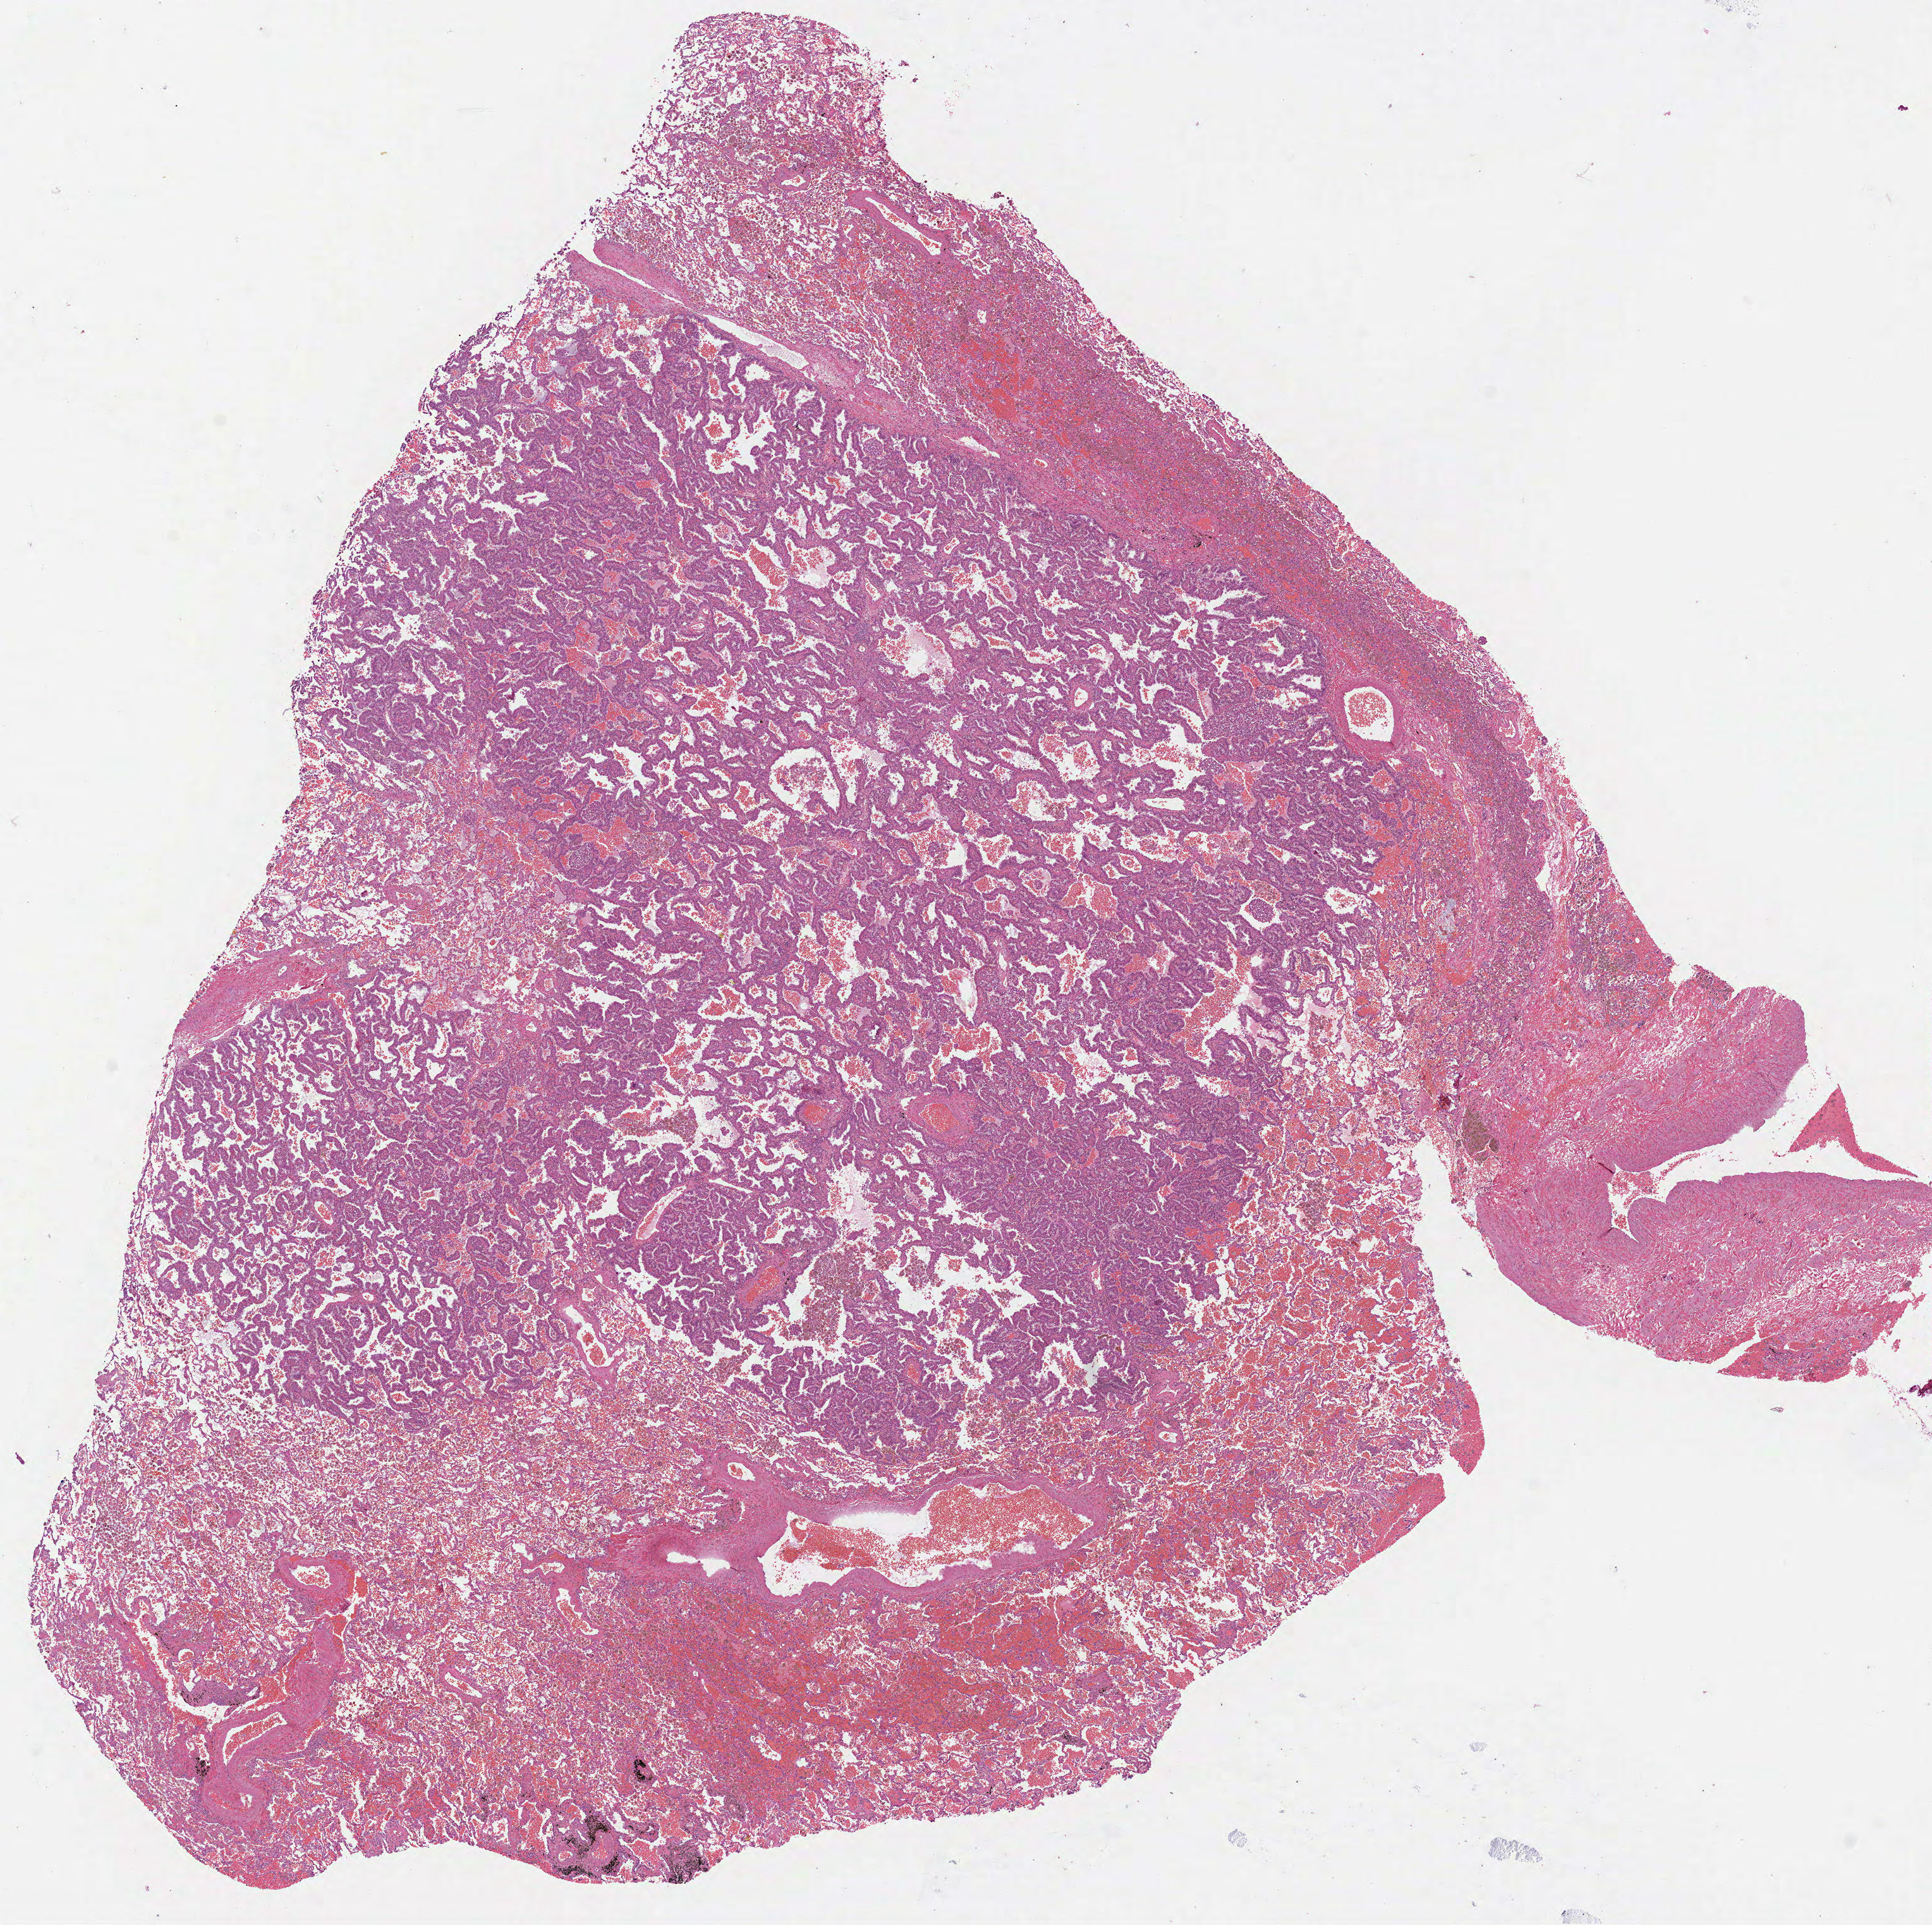
Digitized H&E tissue section (whole slide), whole scanned area (about 12.3 x 12.3 mm, acquisition: 40x scan) shown as a low-resolution overview. FFPE section. Lung, primary tumour sample. Male, age 41 years at initial diagnosis.
Histologic diagnosis: Bronchiolo-alveolar carcinoma, non-mucinous (lower lobe, lung).